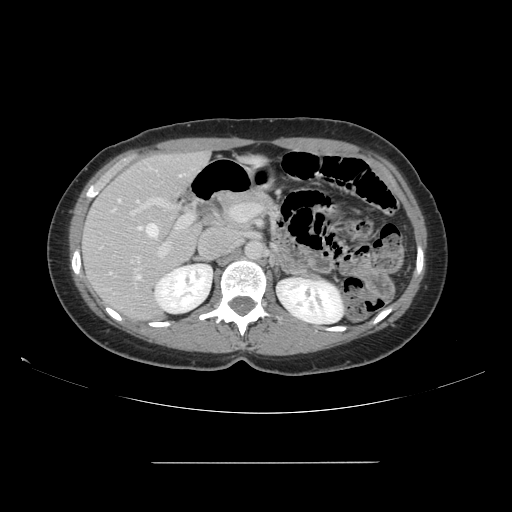
Contrast-enhanced abdominal CT, one axial slice. Position 89 of 151 along the scan axis. Intravenous contrast given. Soft-tissue window (W 400 / L 40 HU). 512 × 512 image matrix. Female patient, age 46 years. Case-level facts recorded for this patient, not image findings: diagnosis: colorectal cancer liver metastases, imaged before liver resection; multiple liver metastases: yes; largest metastasis: 3 cm.
Structures marked on this image (outlined manually by an expert reader):
- hepatic veins: box from (x=112, y=175) to (x=182, y=279) px
- liver: (x=83, y=153)–(x=208, y=322)
- planned liver remnant (the part of the liver to remain after resection): (x=92, y=153)–(x=202, y=284)
- portal vein (with intrahepatic branches): (x=130, y=180)–(x=247, y=273)